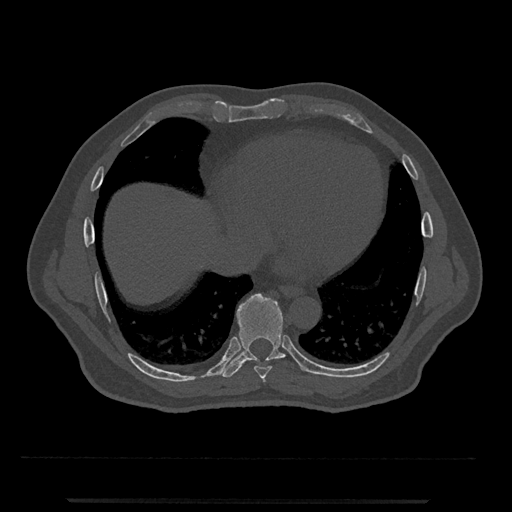
CT including the spine, one axial slice; position 595 of 797 along the scan axis; reconstruction kernel Br40s/3; 120 kVp; bone window (W 1800 / L 400 HU); 0.5 mm slice thickness; 512 × 512 image matrix, field of view 419 × 419 mm. Patient: male, 63 years. From the clinical record (not read from this slice): primary cancer: prostate.
Structures marked on this image (semi-automatic segmentation, software-assisted and operator-edited):
- T7 vertebra: bounding box <263,377,265,382> (left, top, right, bottom; pixels)
- T8 vertebra: <254,361,272,380>
- T9 vertebra: <221,293,286,378>